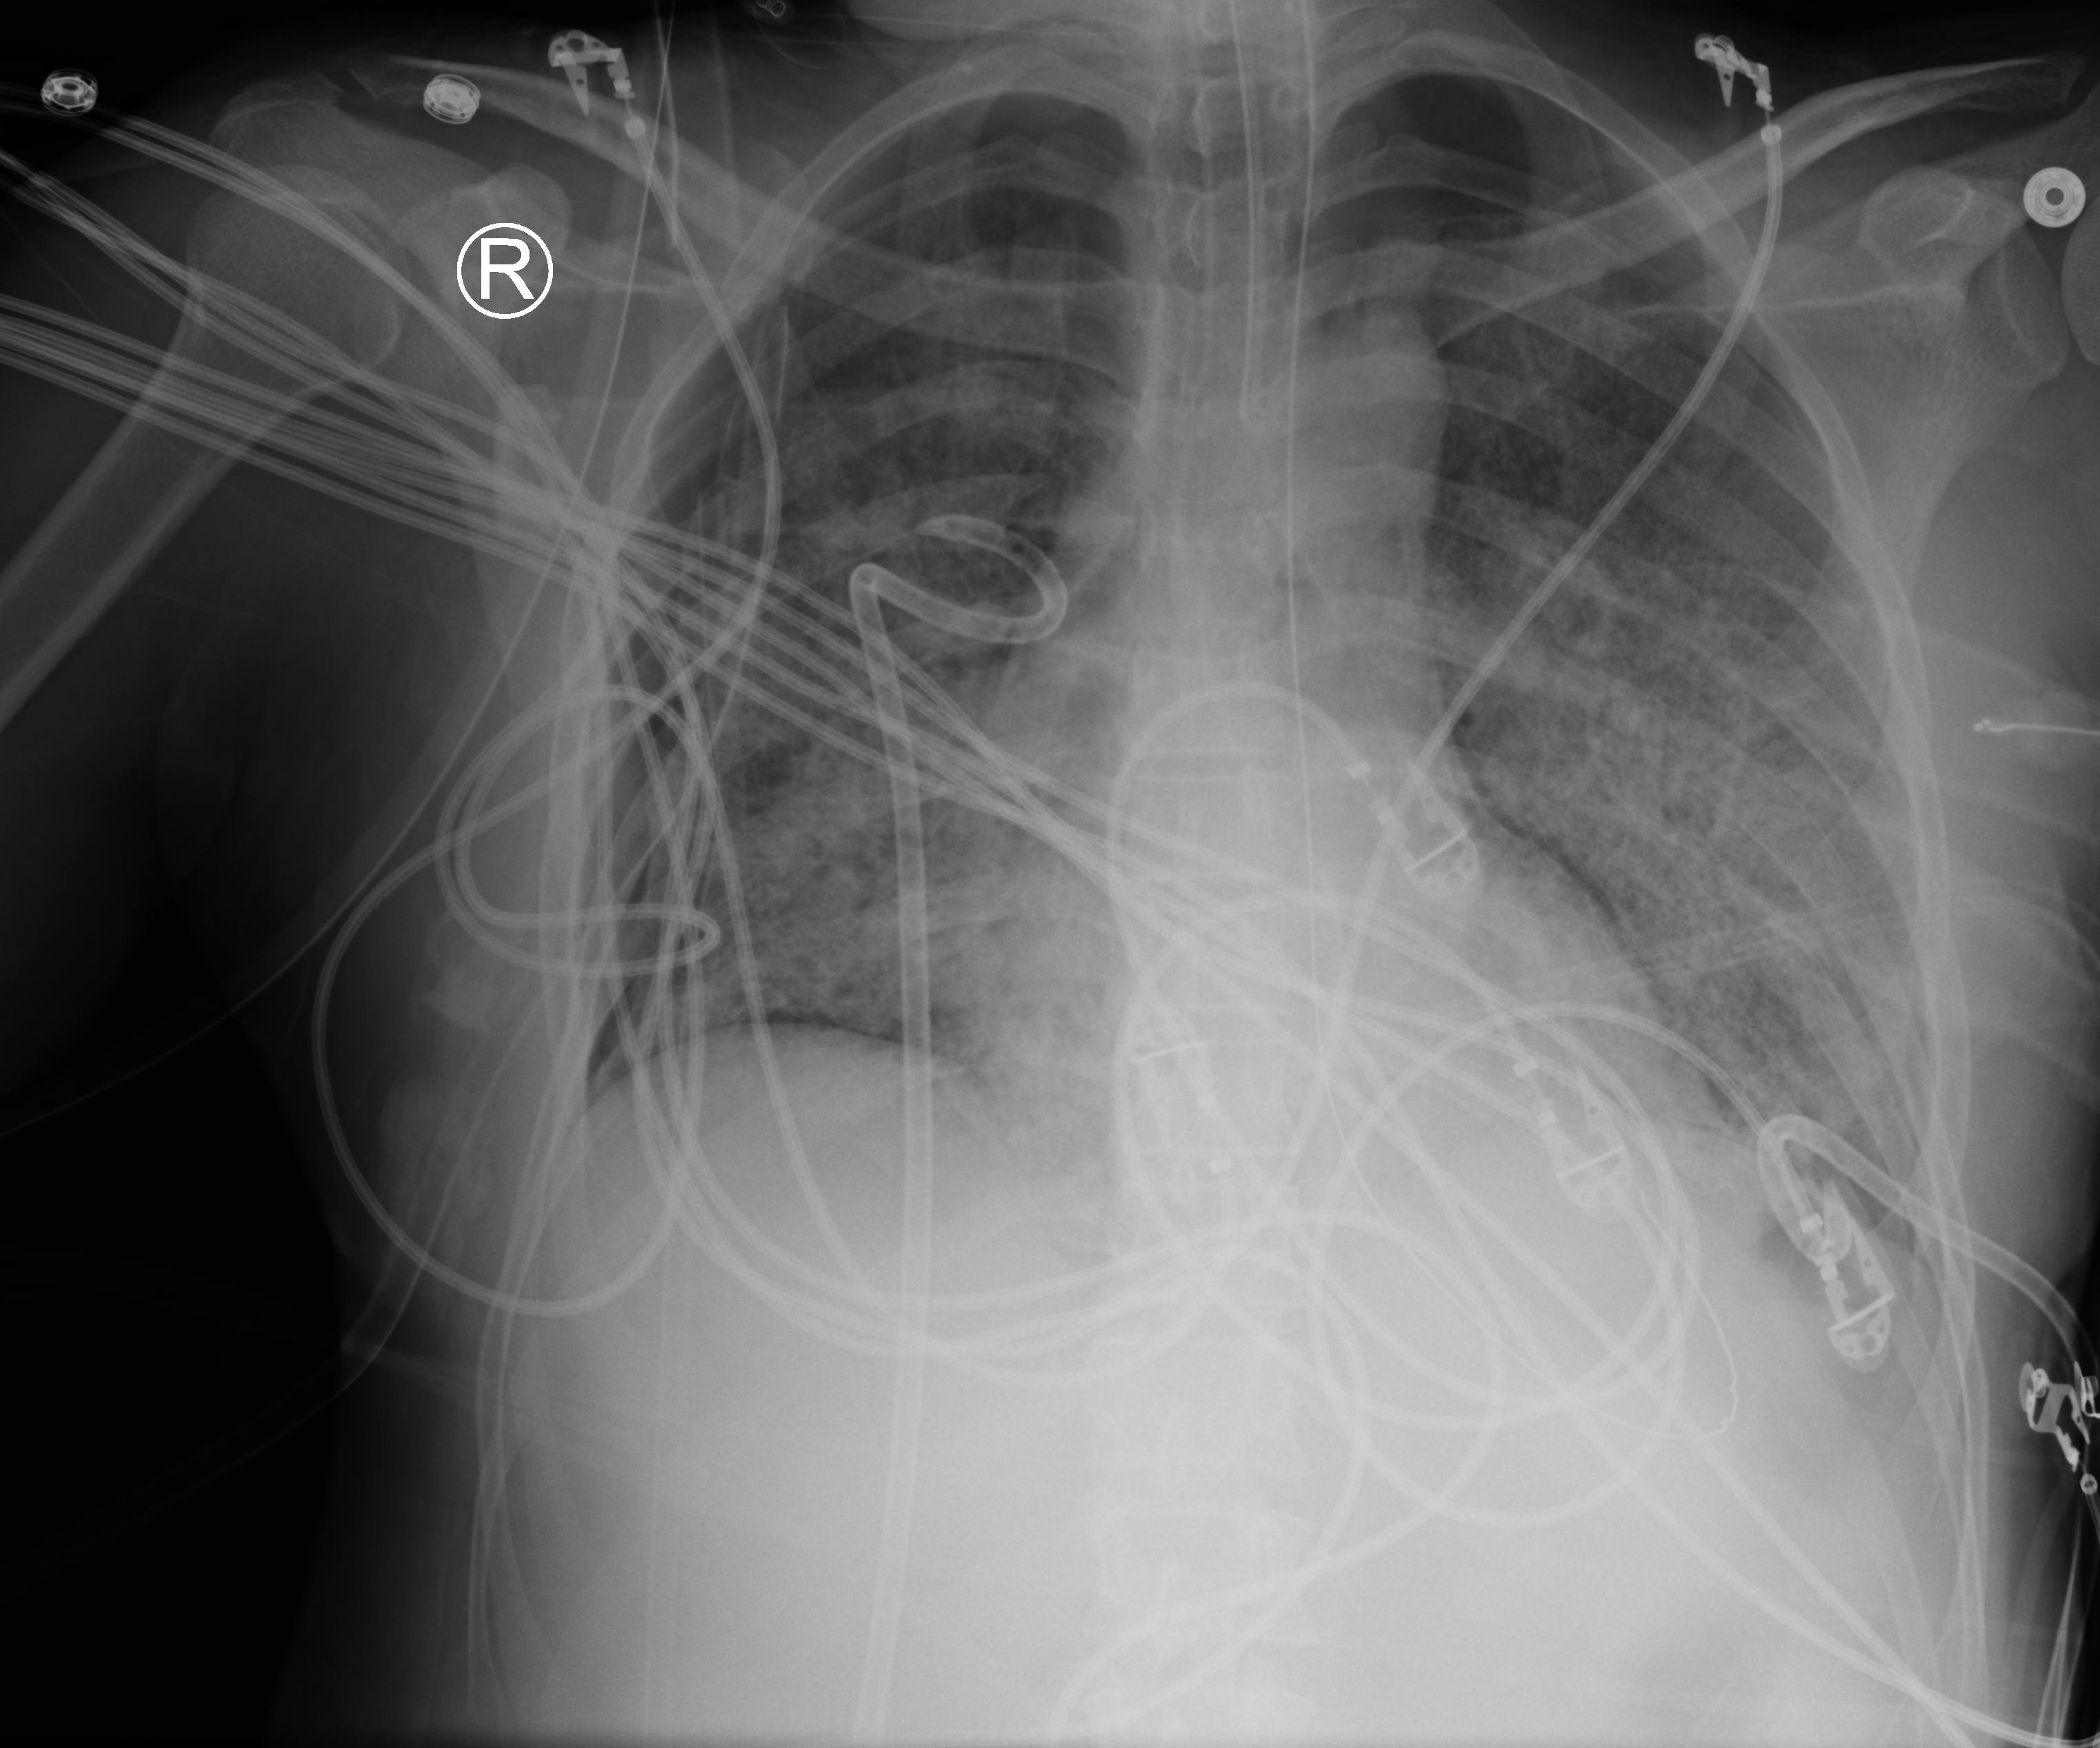
Bedside chest radiograph (computed radiography); anteroposterior (AP) projection. Adult patient hospitalised with COVID-19, age 18–59 years.
Hospital-stay facts (about this admission, not read from this image; timing relative to this image not recorded): admitted to intensive care during this hospital stay: yes; other chronic lung disease (admission record): no.